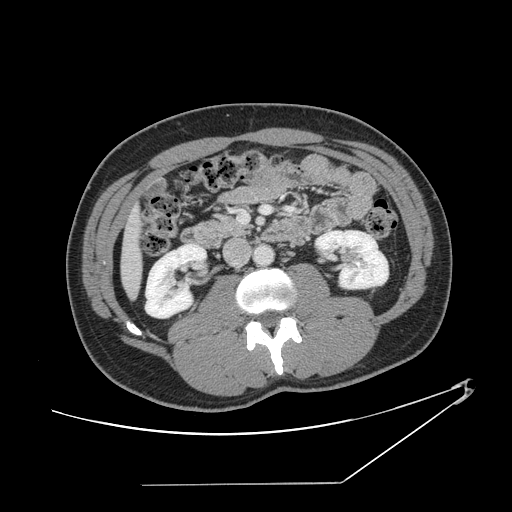
Contrast-enhanced abdominal CT, one axial slice. Slice 47 of 152 in the series (ordered by position). 120 kVp. Intravenous contrast given. Soft-tissue window (W 400 / L 40 HU). 2.5 mm slice thickness. 512 × 512 image matrix. Male patient, age 45 years. From the clinical record (not read from this slice): diagnosis: colorectal cancer liver metastases, imaged before liver resection.
Outlined on this slice (outlined manually by an expert reader):
- liver: bounding box (x1, y1, x2, y2) in pixels: (123, 213, 142, 295)
- planned liver remnant (the part of the liver to remain after resection): (123, 214, 142, 295)
- portal vein (with intrahepatic branches): (239, 206, 293, 223)